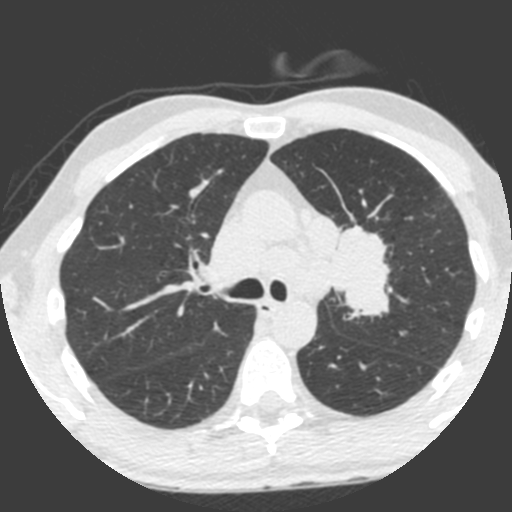
Low-dose screening chest CT, one axial slice. Position 144 of 212 along the scan axis. 120 kVp. Lung window (W 1500 / L -600 HU). 2 mm slice thickness. 512 × 512 image matrix.
Outlined on this slice (manually delineated by an expert):
- lesion 1 (tumor, upper lobe of left lung): bounding box (x1, y1, x2, y2) in pixels: (329, 225, 390, 316)